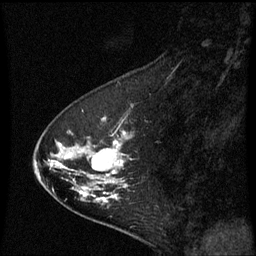
Breast MRI (dynamic contrast-enhanced), one sagittal slice; slice 20 of 60 in the series (ordered by position); dynamic contrast-enhanced series, image 2 of 3 at this slice position (ordered by acquisition); 1.5 T; TE 4.2 ms, TR 8.9 ms; 2 mm slice thickness; 256 × 256 image matrix, field of view 200 × 200 mm. Patient: female, 53 years. From the clinical record (not read from this slice): setting: breast cancer imaged before/during neoadjuvant chemotherapy; receptor status: HR-positive, HER2-negative.
Annotated regions visible in this slice (semi-automatic segmentation, software-assisted and operator-edited):
- analysis volume of interest (the breast-tissue region the enhancement analysis was run in; not a lesion): bounding box [x1, y1, x2, y2] px = [34, 104, 135, 221]
- tumour enhancement mask (voxels above the 70 % enhancement threshold inside the analysis volume of interest): [82, 132, 127, 197]